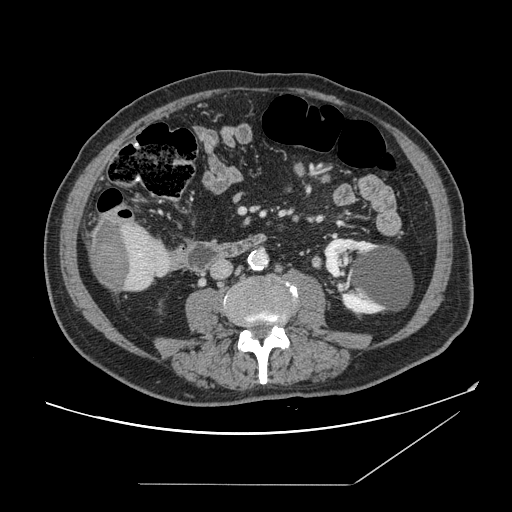
Contrast-enhanced abdominal CT, one axial slice; position 34 of 166 along the scan axis; 120 kVp; intravenous contrast given; soft-tissue window (W 400 / L 40 HU); 2.5 mm slice thickness; 512 × 512 image matrix, field of view 416 × 416 mm. Male patient, age 80 years. From the clinical record (not read from this slice): diagnosis: colorectal cancer liver metastases, imaged before liver resection; multiple liver metastases: no; largest metastasis: 2.2 cm; chemotherapy before resection: no.
Outlined on this slice (manually delineated by an expert):
- liver: bounding box (x1, y1, x2, y2) in pixels: (89, 218, 171, 292)
- liver metastasis: (92, 221, 132, 289)